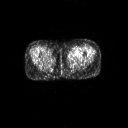
FDG PET of an extremity soft-tissue mass (from a PET/CT study), one axial slice. Position 4 of 267 along the scan axis. 3.27 mm slice thickness. 128 × 128 image matrix. Female patient, age 47 years. From the clinical record (not read from this slice): histological type: myxofibrosarcoma; grade: intermediate; site of the primary tumour: left thigh.
Outlined on this slice (expert contour drawn on MRI and transferred to this co-registered scan by the dataset authors):
- gross tumour volume including surrounding oedema: bounding box [x1, y1, x2, y2] px = [69, 54, 81, 60]